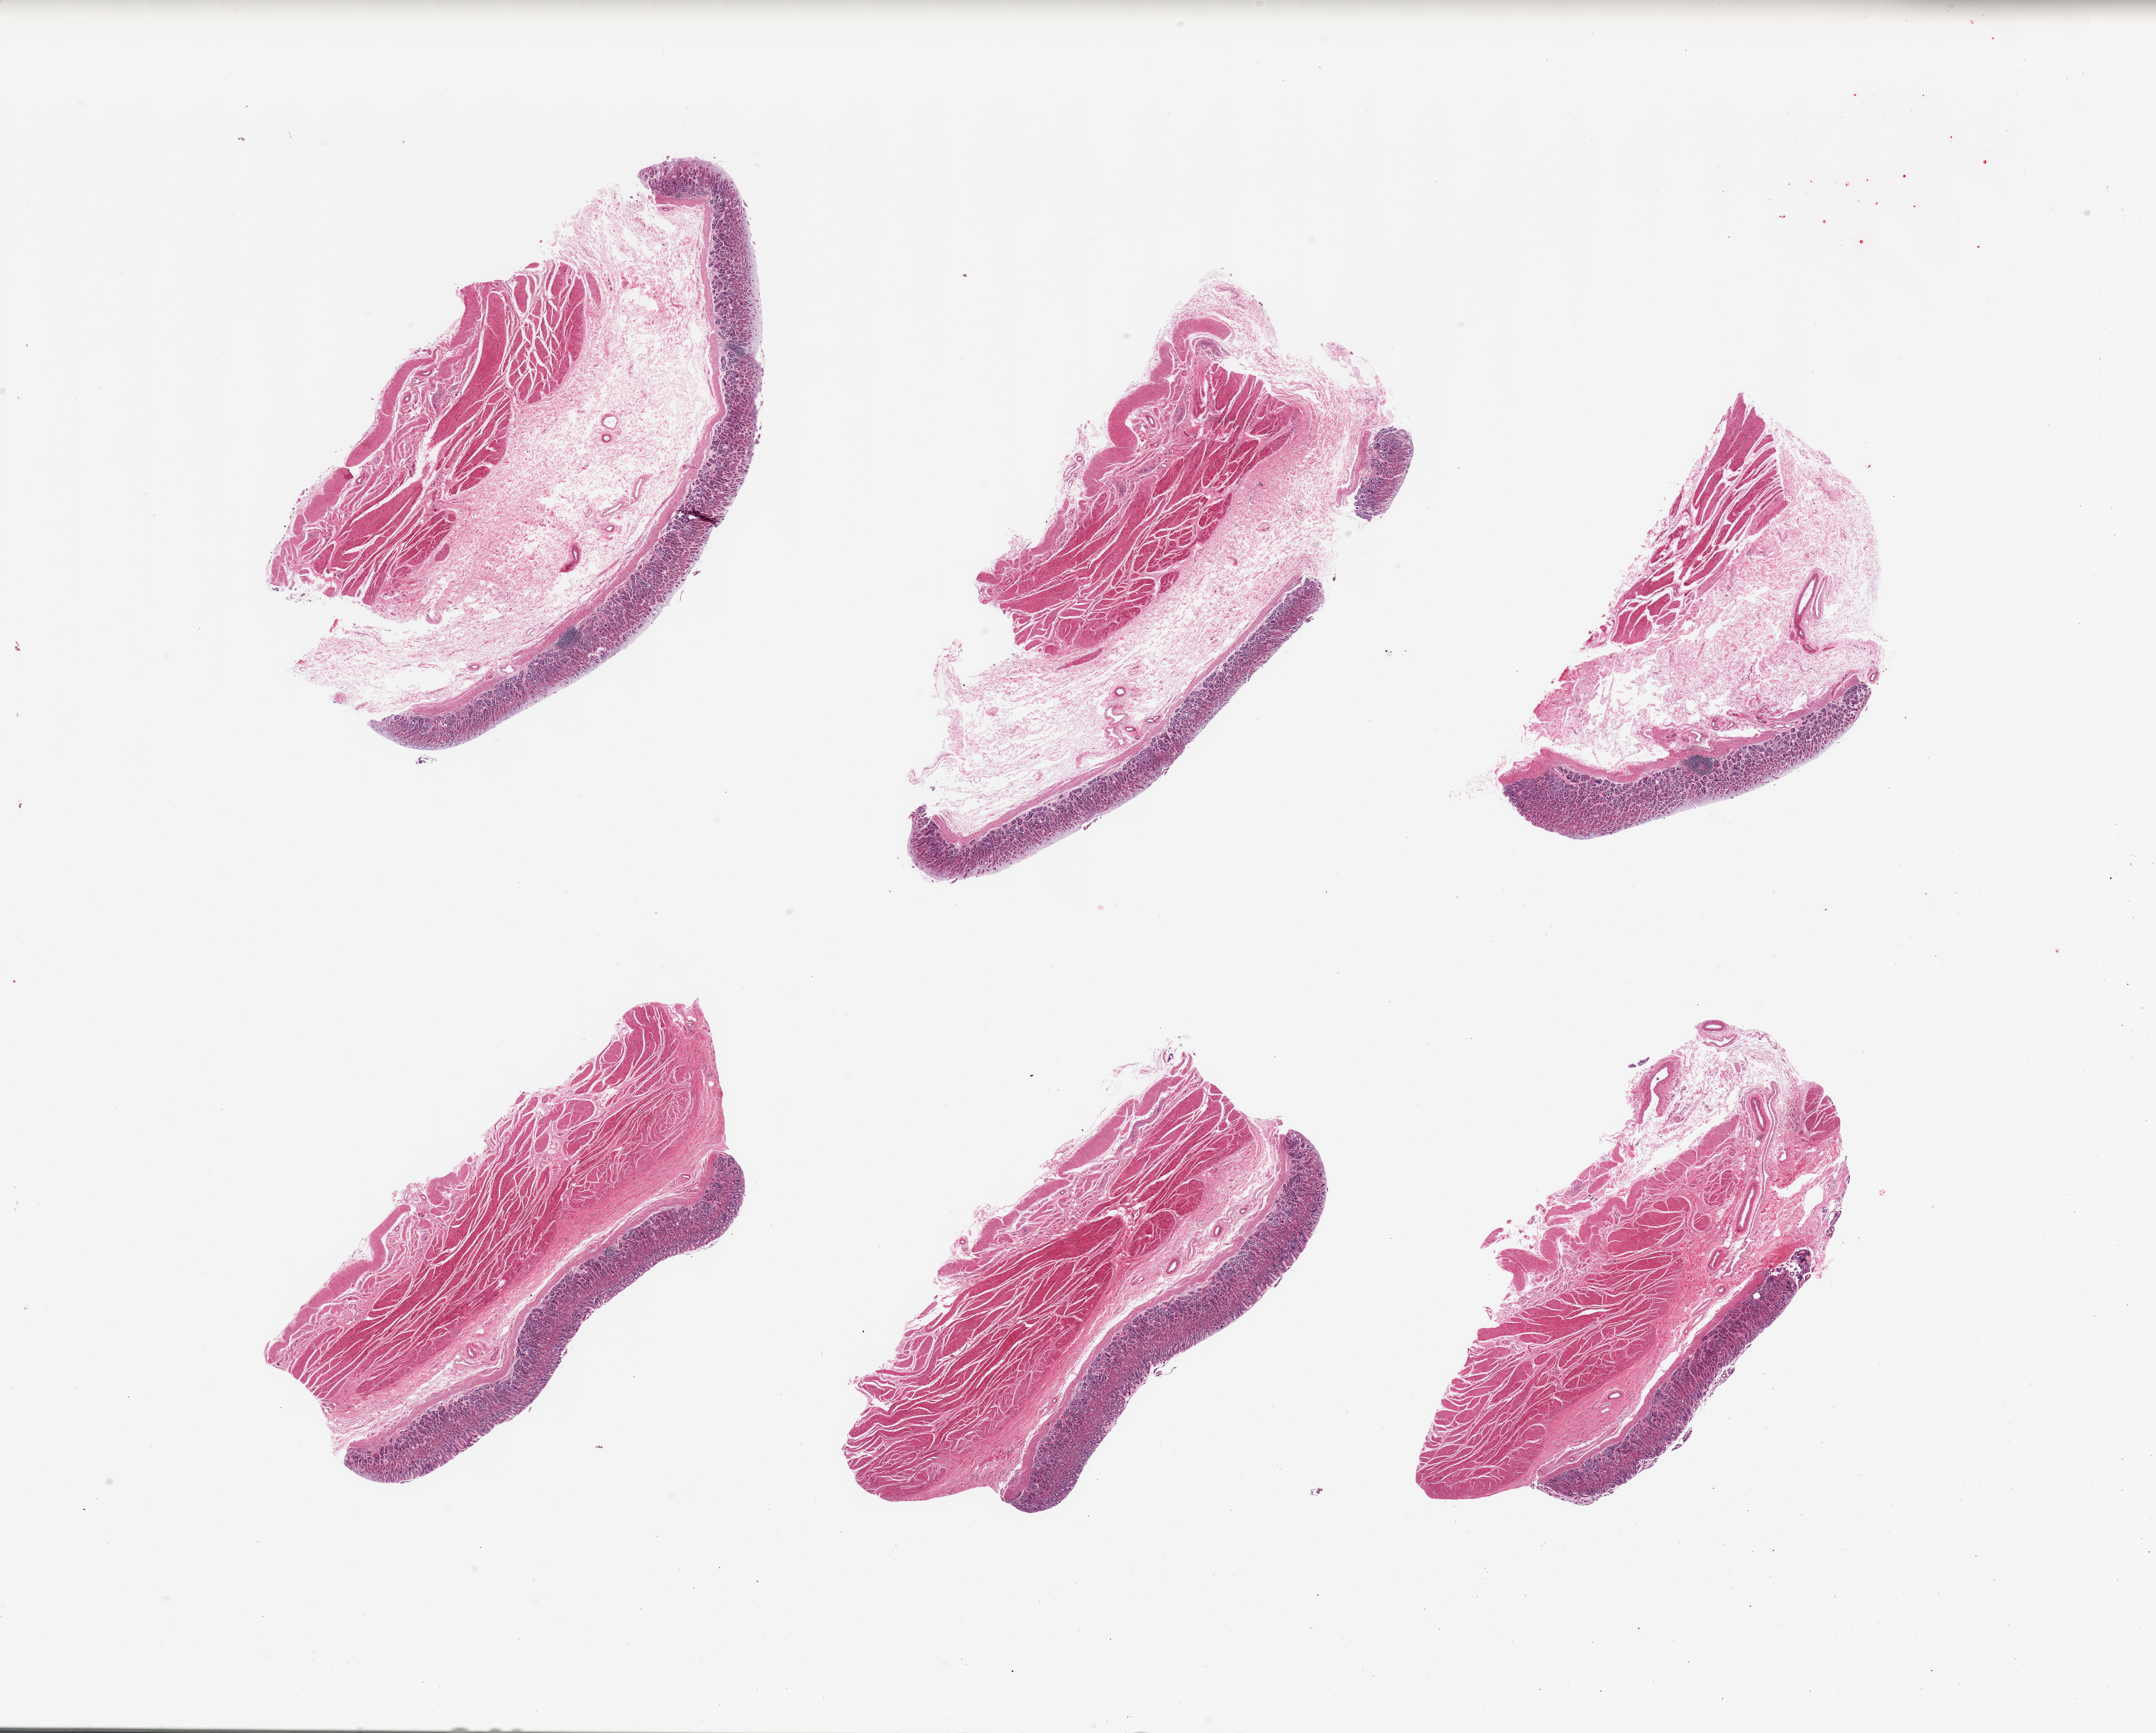
Hematoxylin and eosin (H&E) whole-slide image, shown as a low-resolution overview of the whole scanned area (about 29.5 x 23.7 mm). PAXgene-fixed, paraffin-embedded tissue. Sampled site (target tissue): stomach. Tissue donor sample. Donor sex: female.
• reviewer comment on this tissue sample: 6 pieces, target mucosa up to 0.9m, ~10-20% thickness. Early surface sloughing